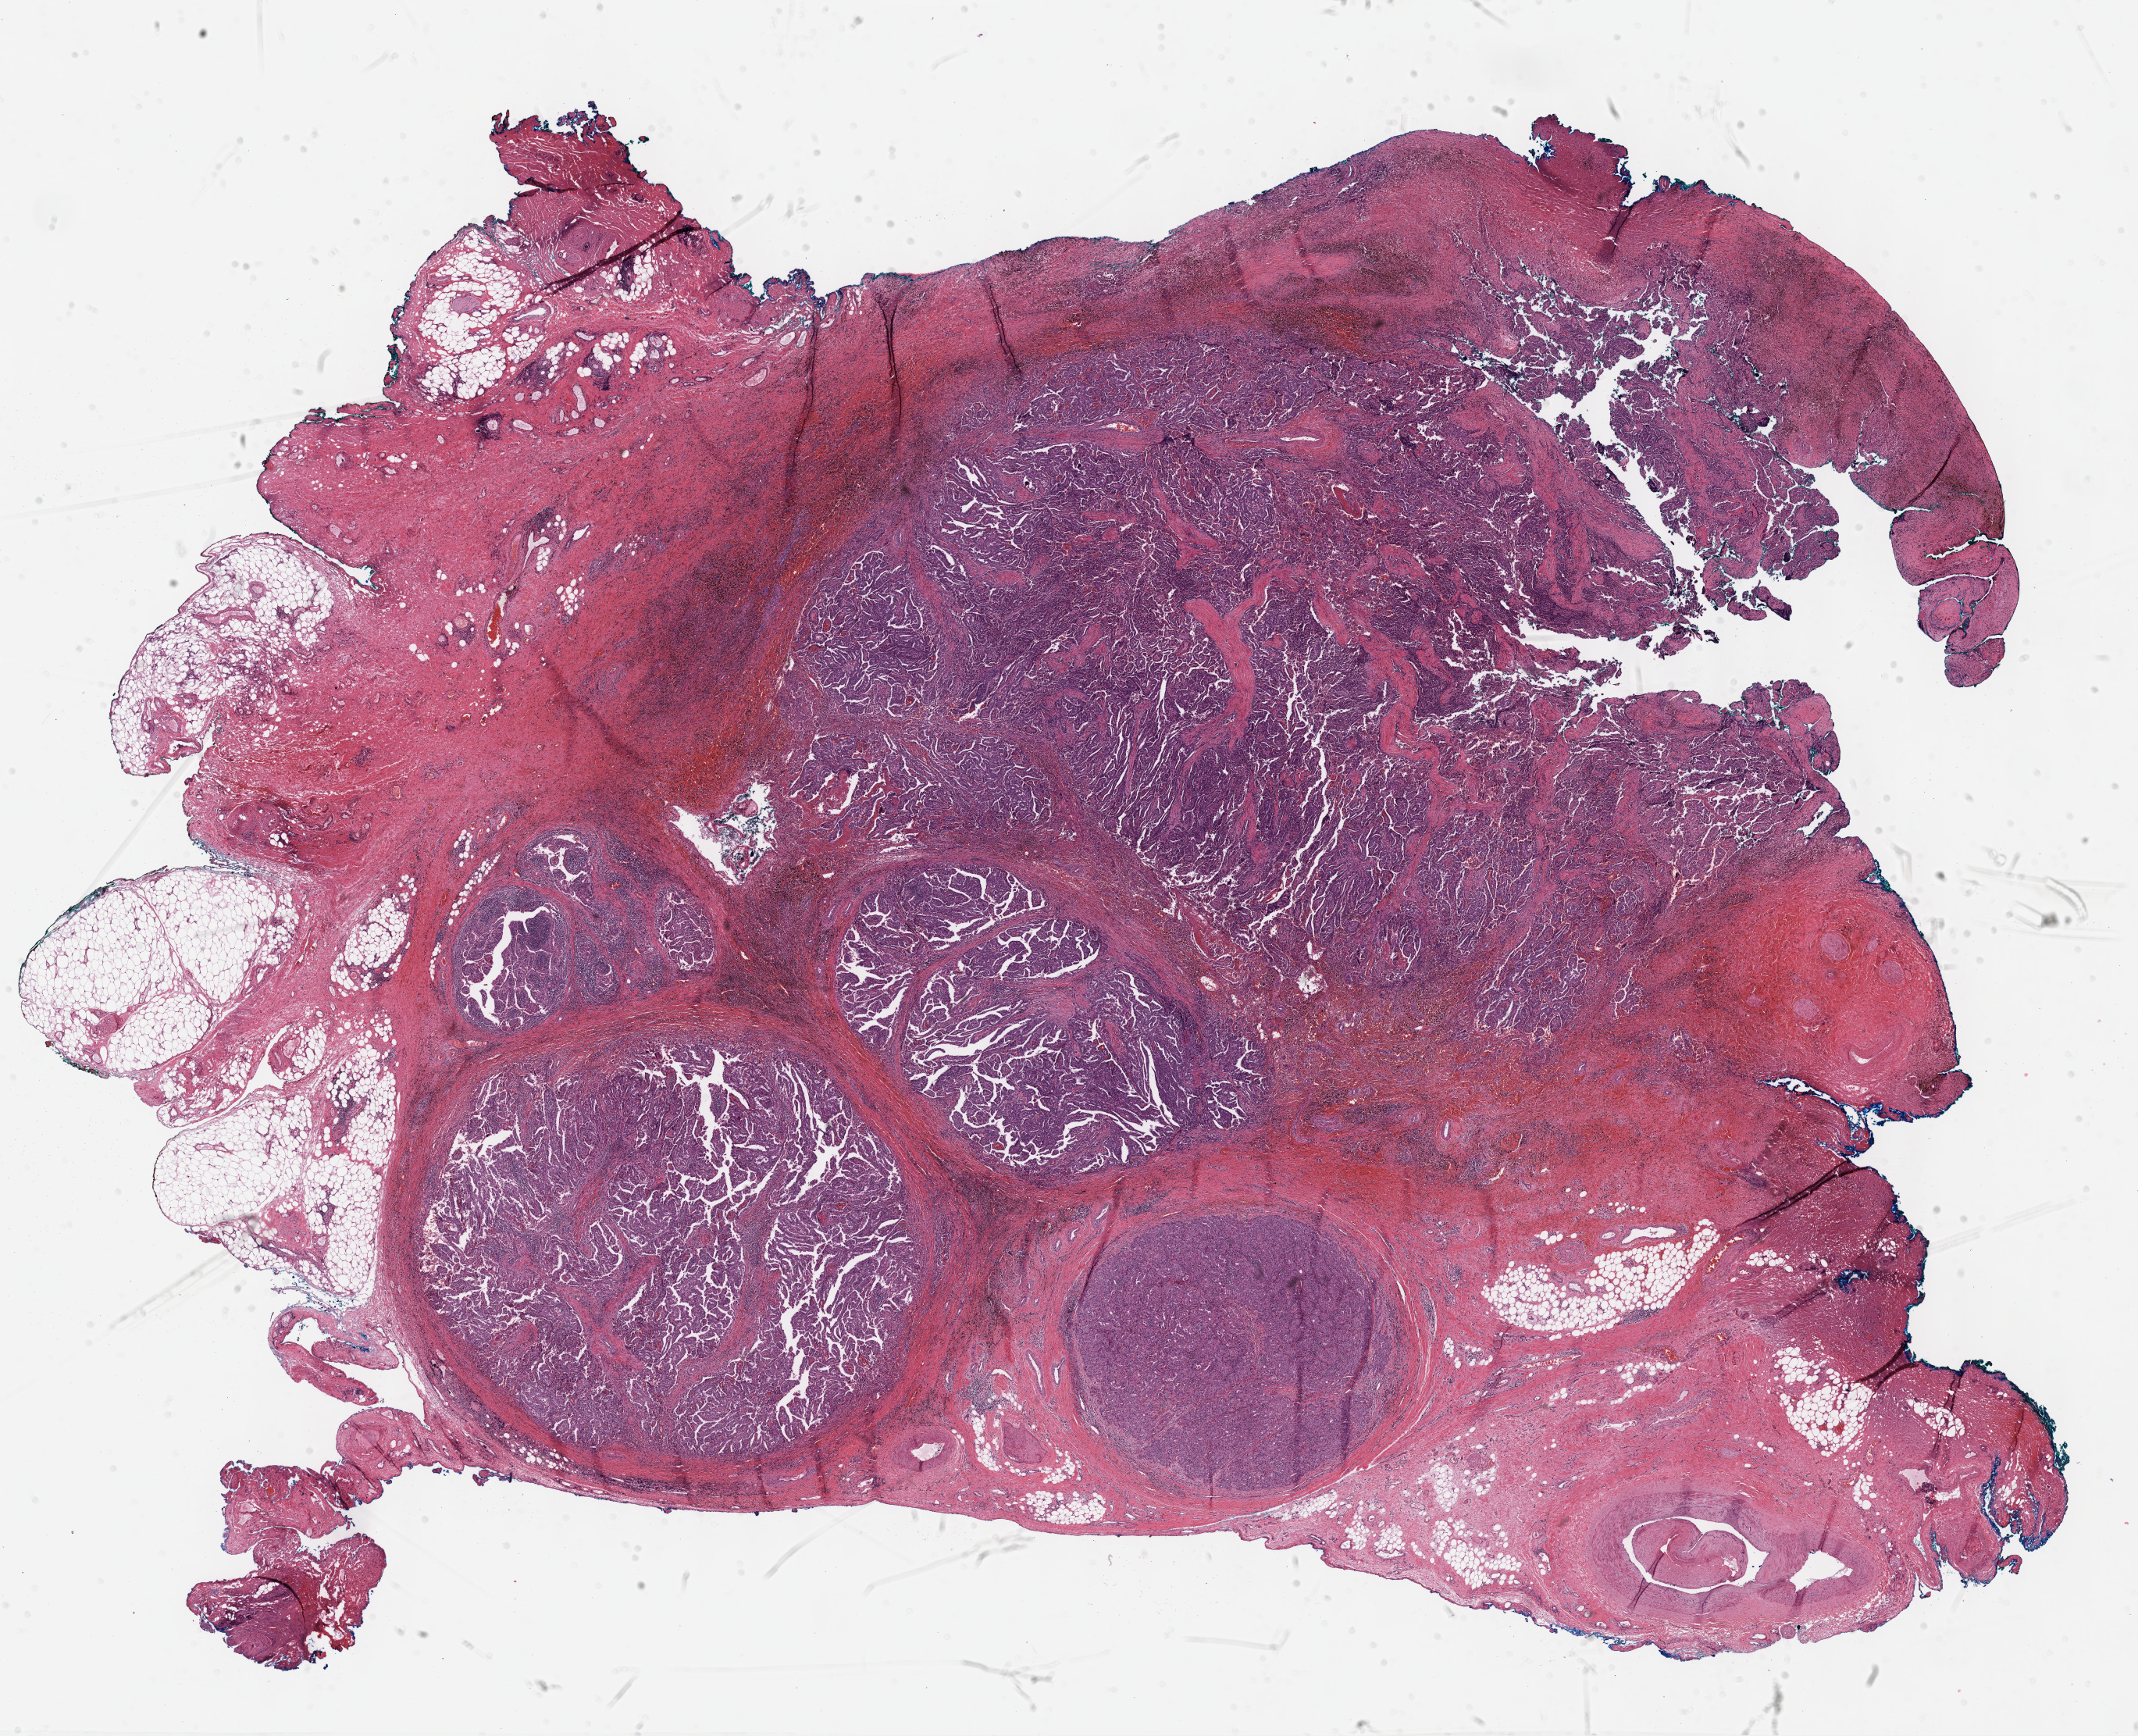
H&E whole-slide image, a low-resolution overview of the entire scanned area, about 22.1 x 18.0 mm (slide scanned at 40x). Formalin-fixed paraffin-embedded (FFPE) diagnostic section. Primary tumour sample from the thyroid. Female, age 74 years at initial diagnosis.
Histologic diagnosis: Papillary carcinoma, NOS (thyroid gland). AJCC pathologic stage: IVA (7th edition).